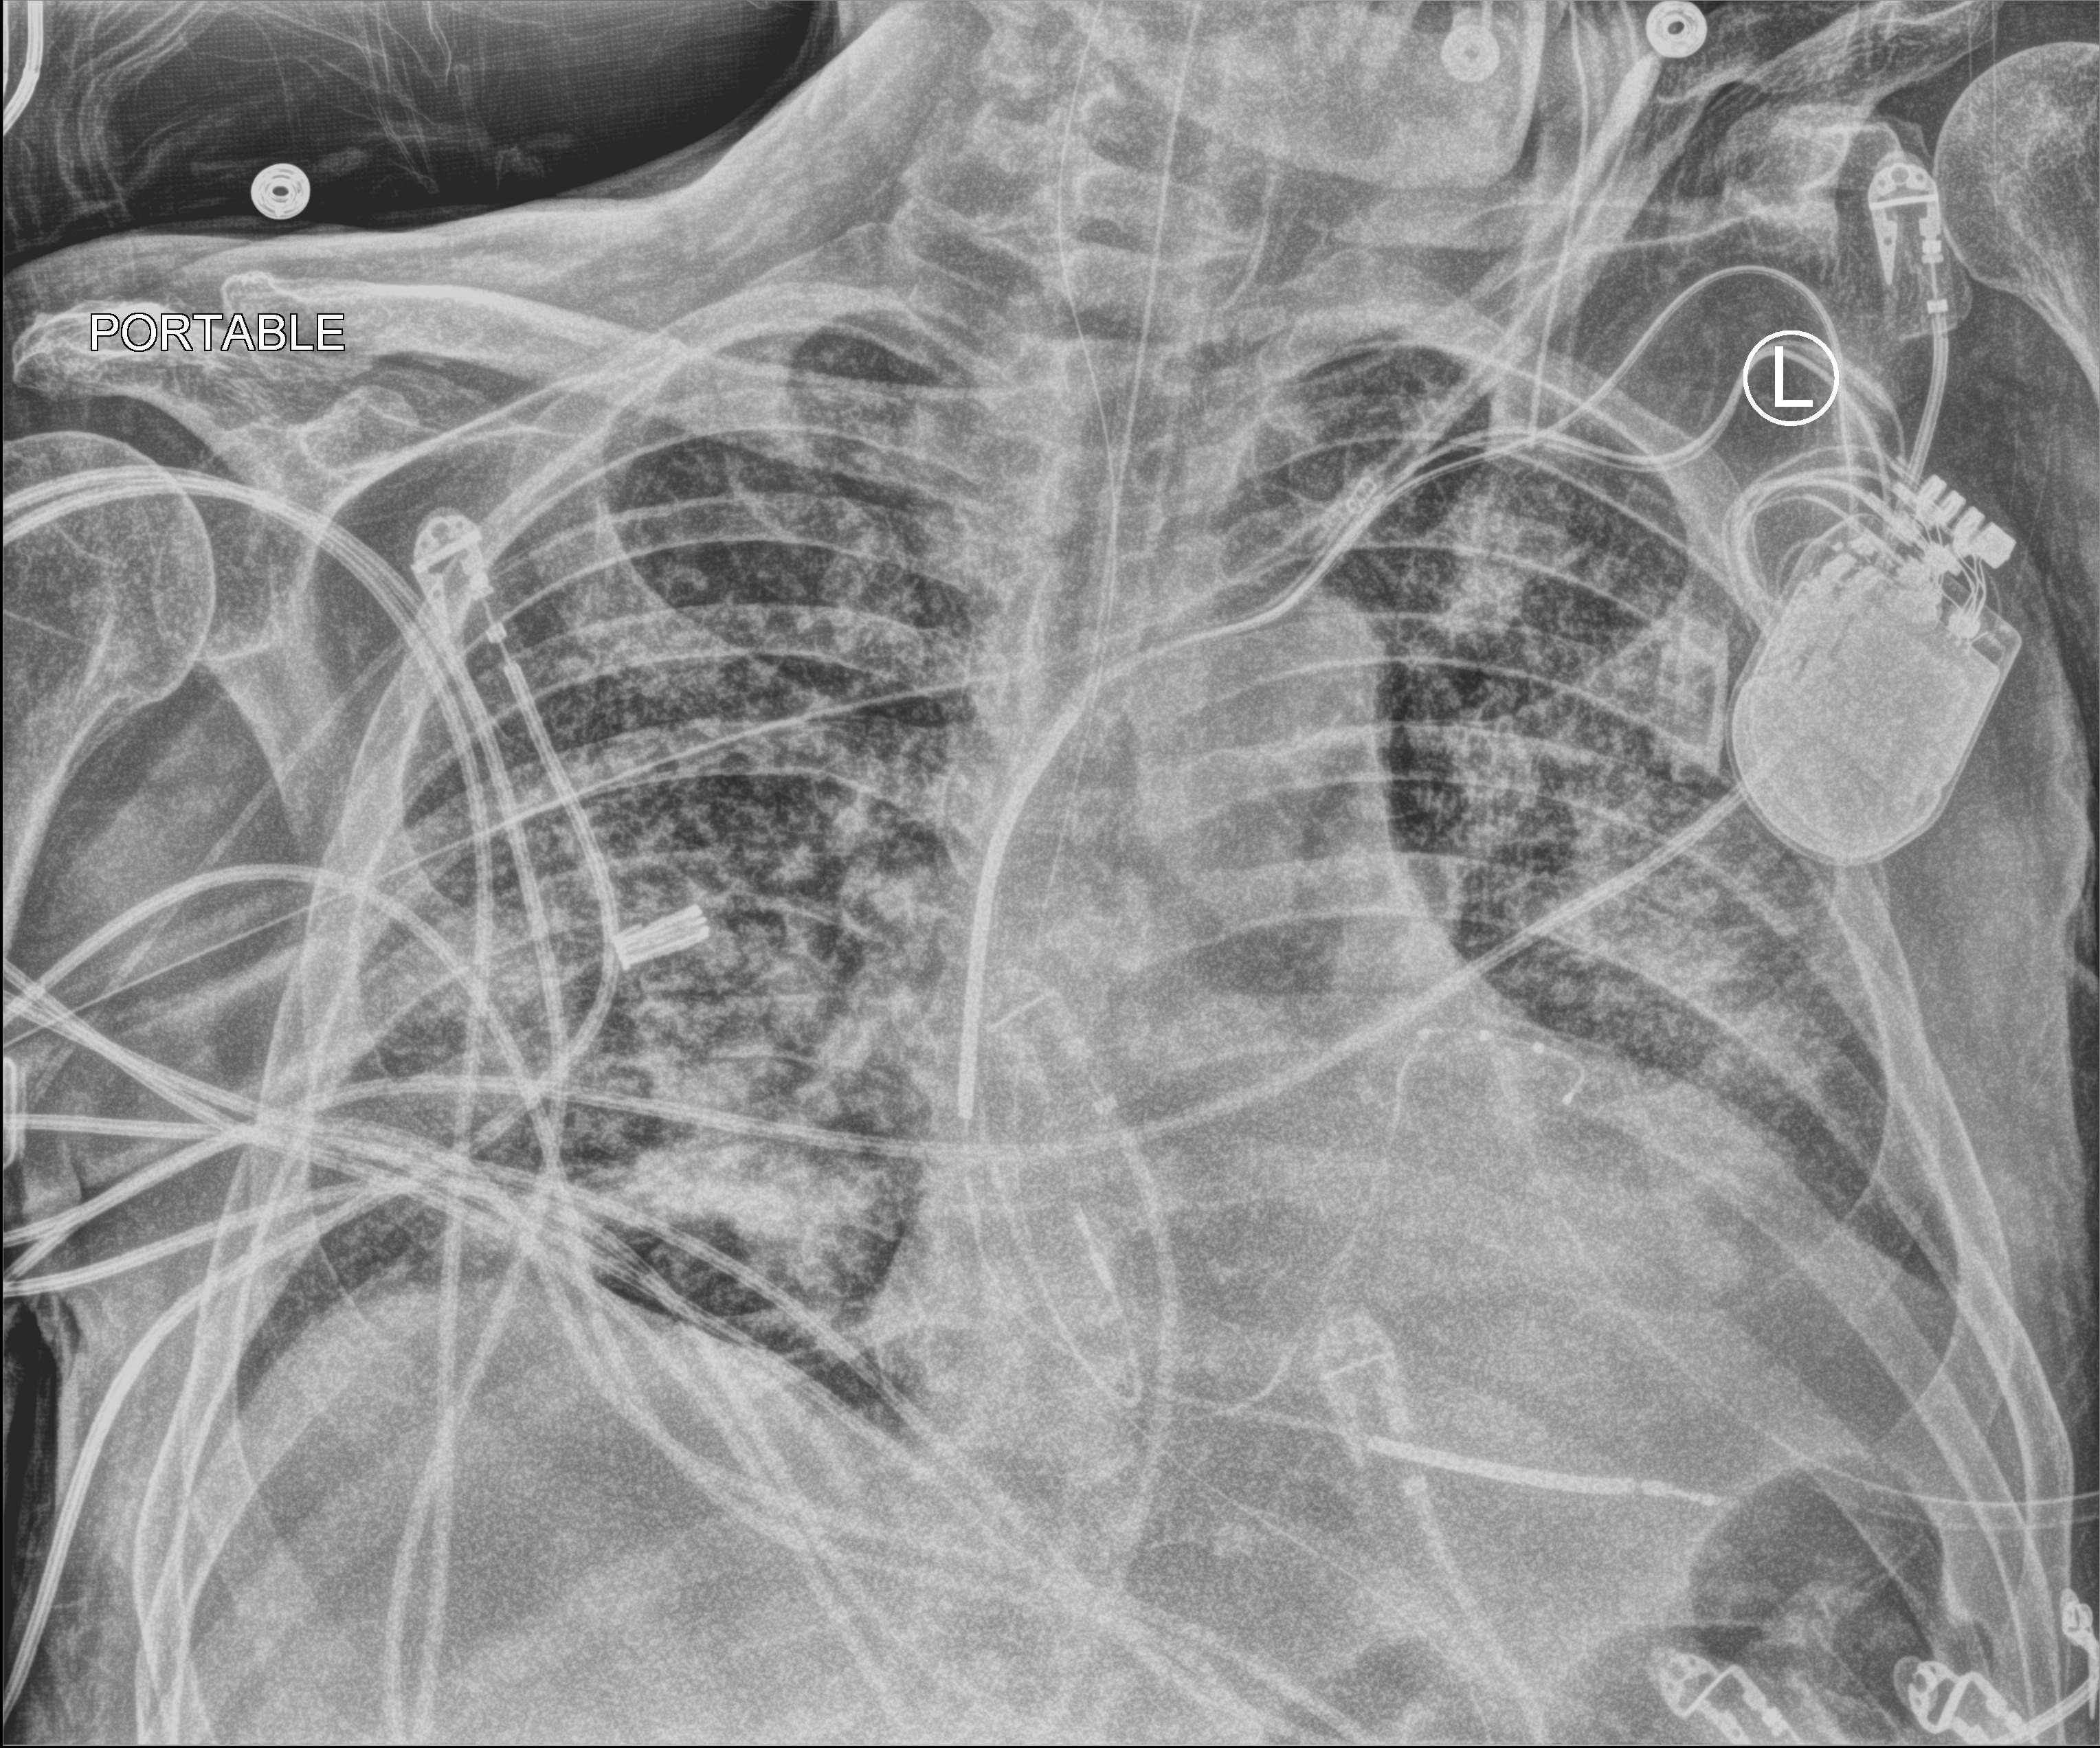
Bedside chest radiograph (computed radiography), anteroposterior (AP) projection. Male patient hospitalised with COVID-19, age 60–74 years.
Hospital-stay facts (about this admission, not read from this image; timing relative to this image not recorded):
- other chronic lung disease (admission record): no
- mechanically ventilated during this hospital stay: yes
- admitted to intensive care during this hospital stay: yes